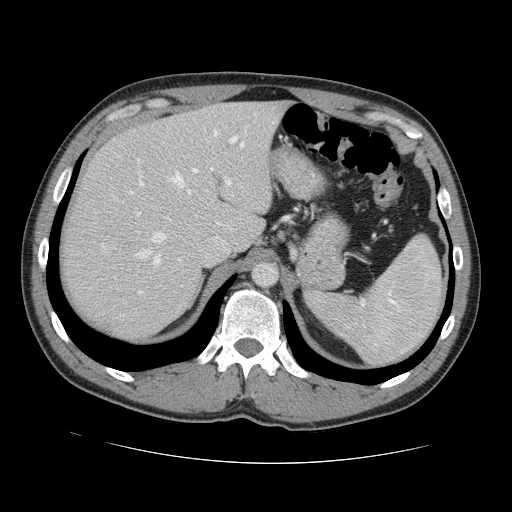
Contrast-enhanced abdominal CT, one axial slice. Position 98 of 131 along the scan axis. Intravenous contrast given. Soft-tissue window (W 400 / L 40 HU). 512 × 512 image matrix, field of view 380 × 380 mm. Male patient, age 40 years. From the clinical record (not read from this slice): diagnosis: colorectal cancer liver metastases, imaged before liver resection; multiple liver metastases: yes; largest metastasis: 2.9 cm.
Annotated regions visible in this slice (expert manual segmentation):
- hepatic veins: bounding box [x1, y1, x2, y2] px = [122, 143, 244, 316]
- liver: [63, 102, 284, 338]
- planned liver remnant (the part of the liver to remain after resection): [98, 102, 285, 249]
- portal vein (with intrahepatic branches): [192, 136, 238, 186]
- liver metastasis: [105, 324, 112, 331]